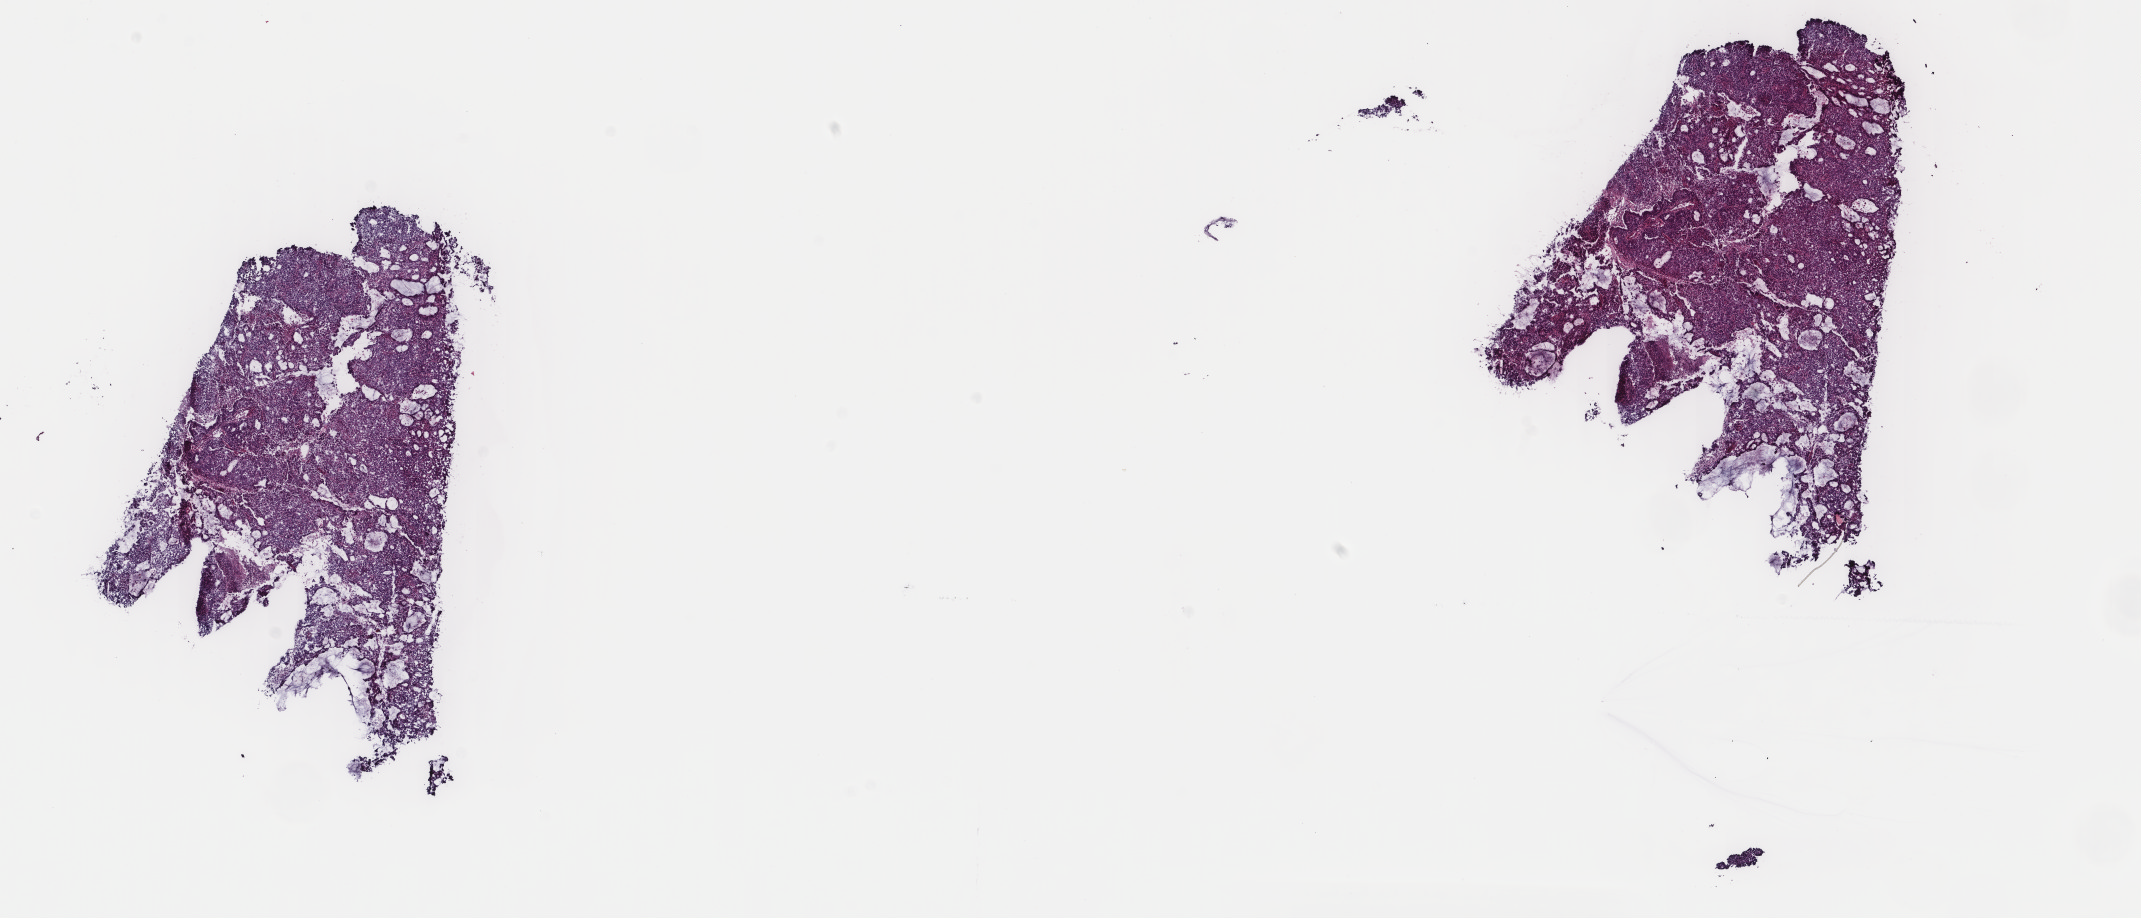
H&E whole-slide image, low-resolution overview of the scanned area, about 17.0 x 7.3 mm (from a 40x scan), frozen section from the top of the tissue portion, primary tumour sample from the uterus. Patient: female, age at initial diagnosis 74 years. Histologic grade: G3 (poorly differentiated). Composition of this section per pathologist review: tumour cells 85%, tumour nuclei 80%, normal cells 0%, stromal cells 0%, necrosis 15%. Infiltration values recorded for this section: lymphocyte infiltration 1%, monocyte infiltration 5%, neutrophil infiltration 2%.
* FIGO stage: IA
* diagnosis: Endometrioid adenocarcinoma, NOS